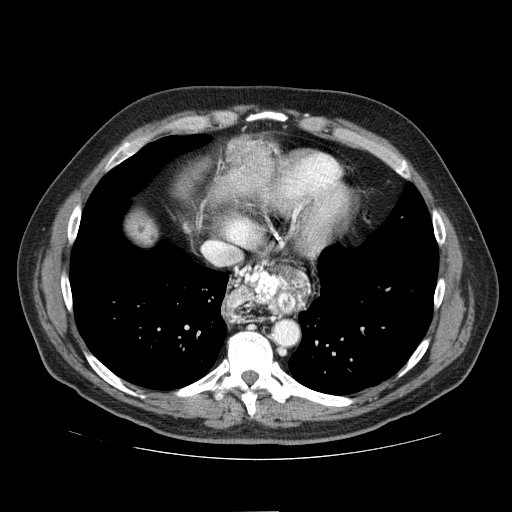
Contrast-enhanced abdominal CT (liver protocol), one axial slice. Slice 69 of 81 in the series (ordered by position). Reconstruction kernel STANDARD. 100 kVp. One of 2 acquisitions stored at this slice position. Soft-tissue window (W 400 / L 40 HU). 2.5 mm slice thickness. 512 × 512 image matrix. Case-level facts recorded for this patient, not image findings: diagnosis: hepatocellular carcinoma (patient treated with transarterial chemoembolisation; whether this scan precedes or follows treatment is not stated here); TNM stage (as recorded): Stage-IIIA; Child-Pugh class: A; tumour nodularity: multinodular; tumour size: 5.6 cm.
Structures marked on this image (semi-automatic segmentation, software-assisted and operator-edited):
- liver parenchyma outside the tumour (the mass and vessels are separate outlines, so this box may not span the whole liver): bounding box [x1, y1, x2, y2] px = [128, 216, 156, 244]
- mass: [230, 139, 271, 180]